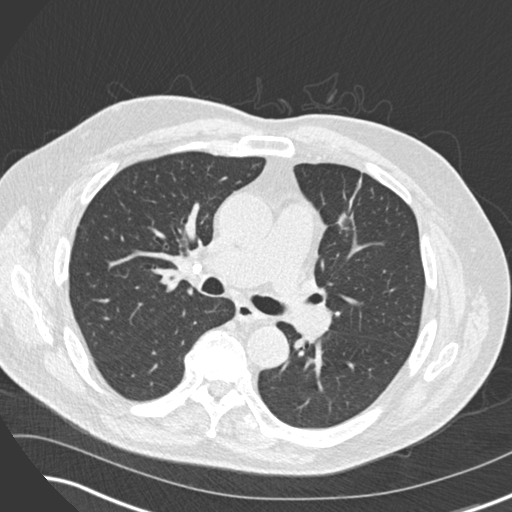
Low-dose screening chest CT, one axial slice; position 98 of 169 along the scan axis; reconstruction kernel B30f; 120 kVp; lung window (W 1500 / L -600 HU); 512 × 512 image matrix, field of view 360 × 360 mm.
Outlined on this slice (manually delineated by an expert):
- lesion 1 (tumor, upper lobe of left lung): bounding box [x1, y1, x2, y2] px = [338, 214, 353, 226]